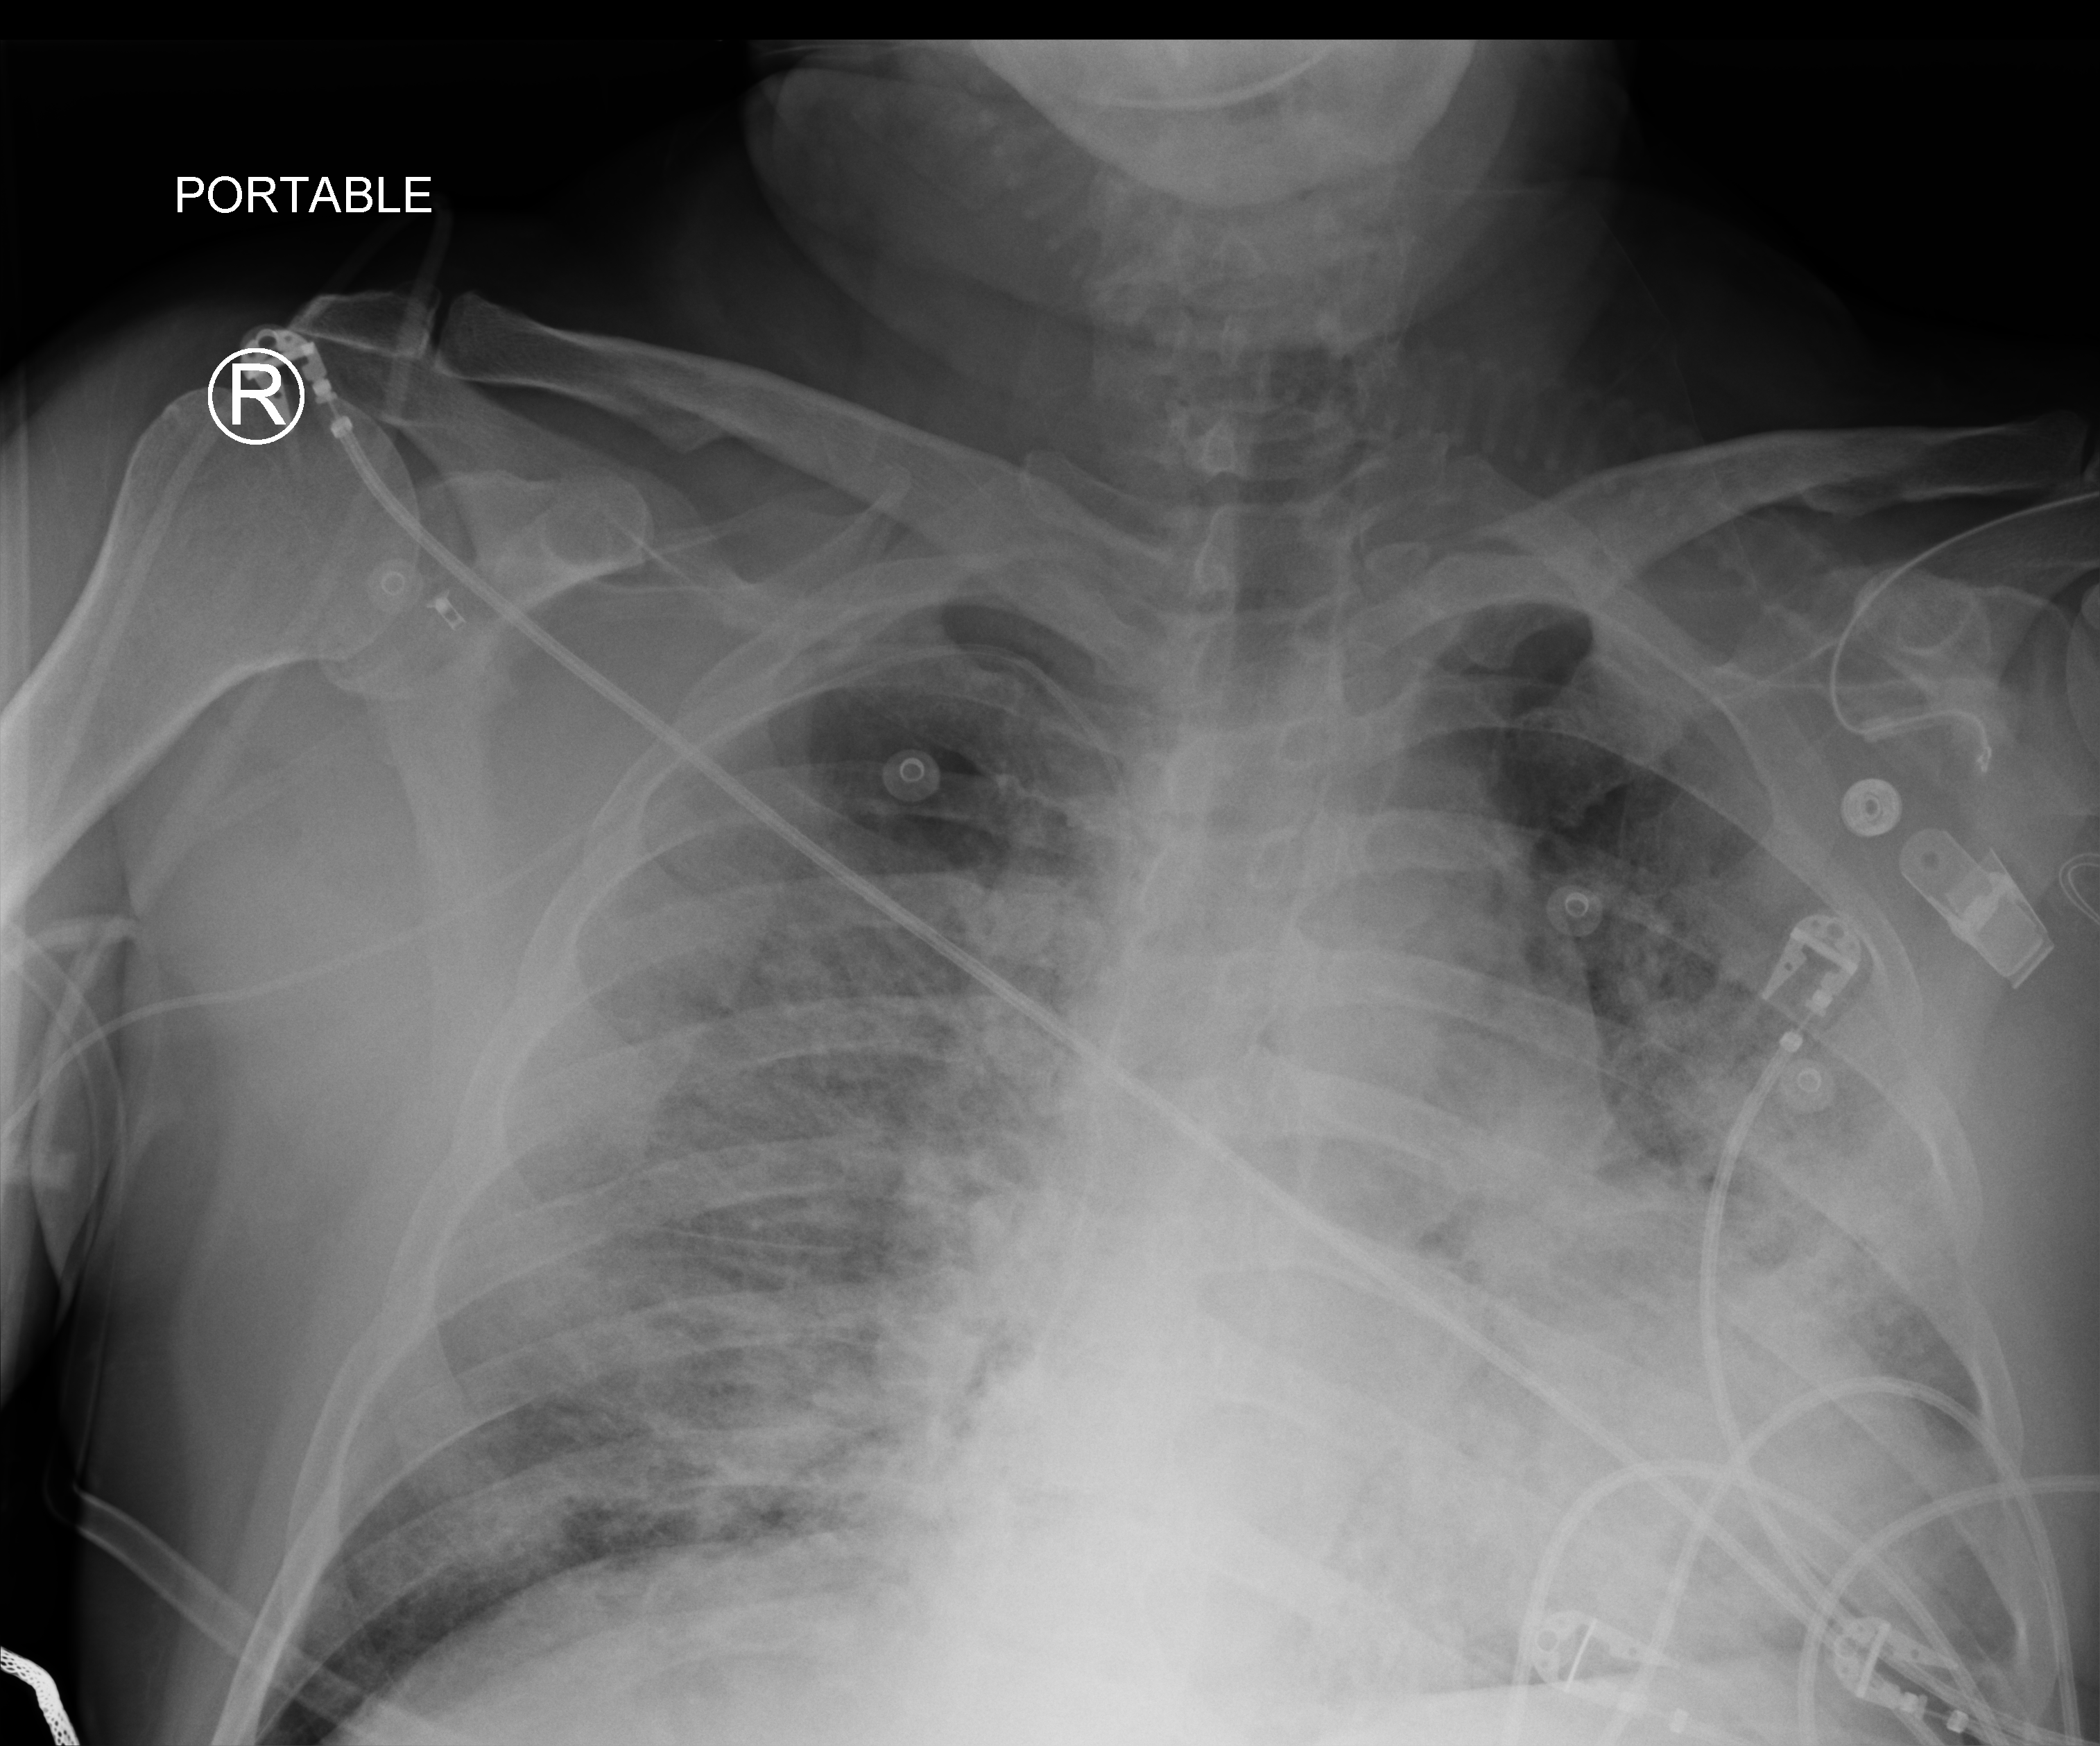
Chest X-ray (portable). Male patient hospitalised with COVID-19, age 18–59 years.
Hospital-stay facts (about this admission, not read from this image; timing relative to this image not recorded): admitted to intensive care during this hospital stay: yes.